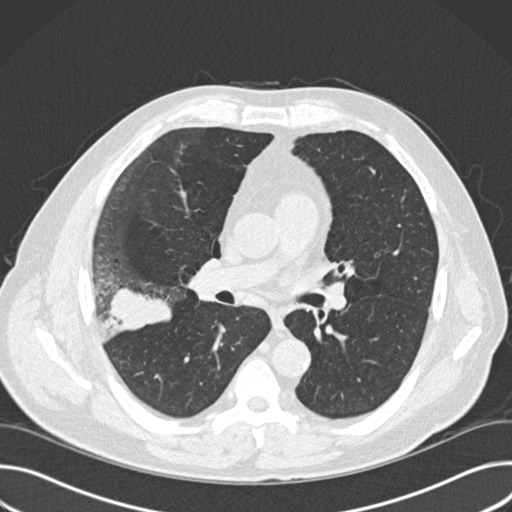
Low-dose screening chest CT, one axial slice; position 92 of 157 along the scan axis; 120 kVp; lung window (W 1500 / L -600 HU); 2 mm slice thickness; 512 × 512 image matrix.
Annotated regions visible in this slice (expert manual segmentation):
- lesion 1 (tumor, upper lobe of right lung): bounding box <107,288,172,330> (left, top, right, bottom; pixels)